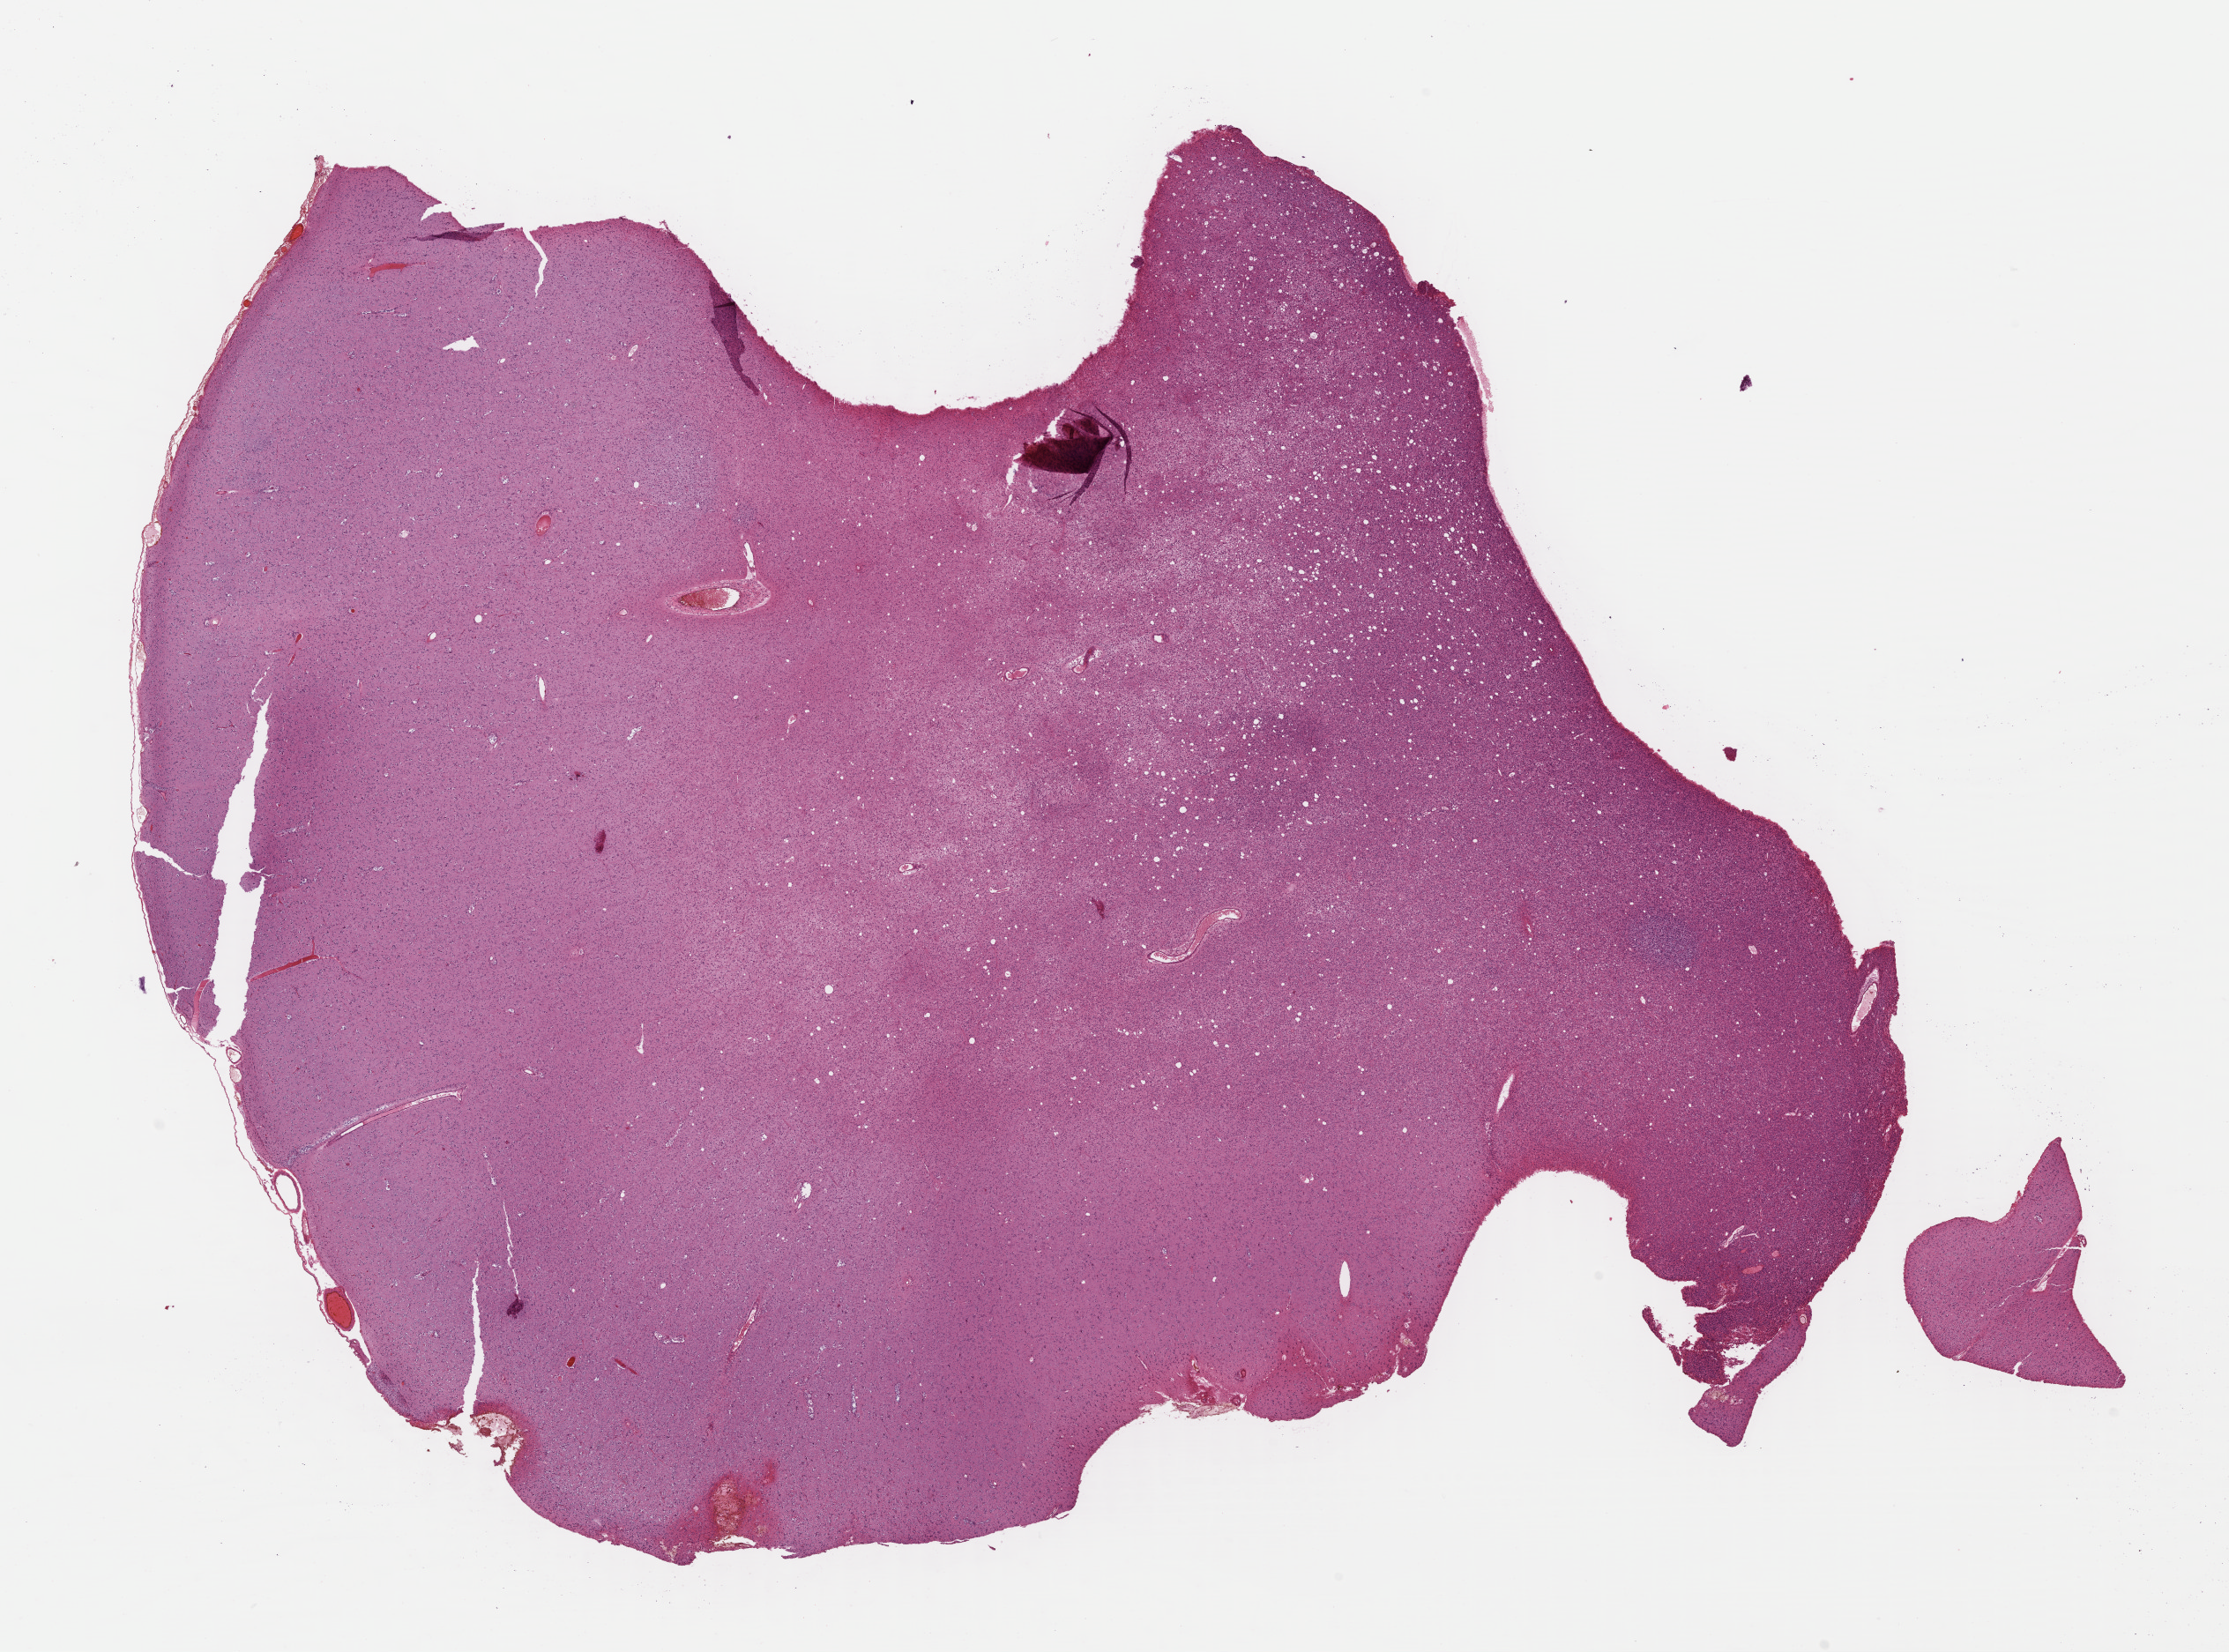
Whole-slide histology image, H&E, low-resolution overview of the scanned area, about 19.9 x 14.7 mm (slide scanned at 40x). Formalin-fixed paraffin-embedded (FFPE) diagnostic section. Sample: primary tumour, brain. Patient: female, age at initial diagnosis 20 years. Histologic grade: G2 (moderately differentiated).
- laterality: left
- histologic diagnosis: Oligodendroglioma, NOS